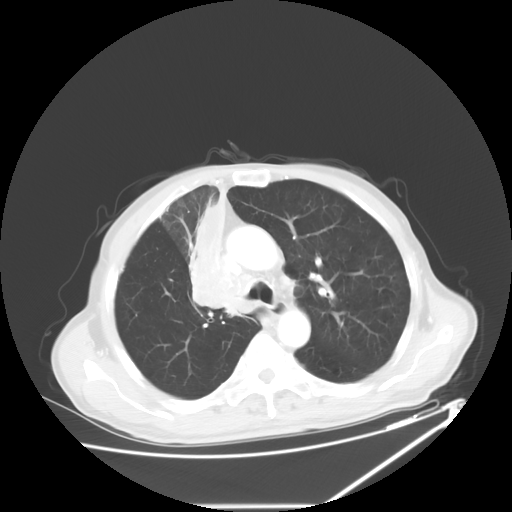
Chest CT, one axial slice. Slice 42 of 60 in the series (ordered by position). 120 kVp. Lung window (W 1500 / L -600 HU). 512 × 512 image matrix, field of view 410 × 410 mm. Male patient, age 73 years. Case-level facts recorded for this patient, not image findings: clinical TNM (as recorded): T2a N1 M0.
Outlined on this slice (bounding box drawn by a radiologist):
- lung tumour (recorded histology: squamous cell carcinoma): box from (x=187, y=185) to (x=235, y=321) px